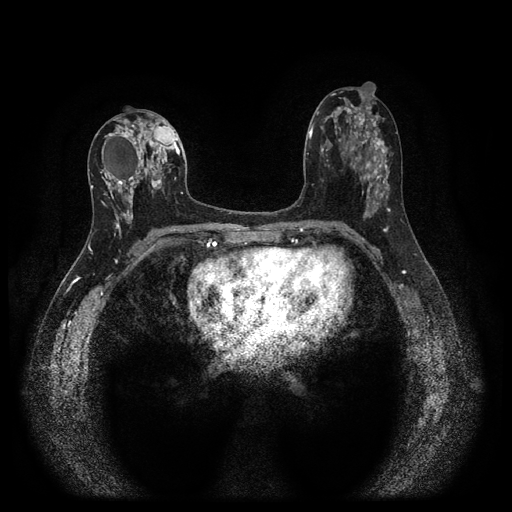
Breast MRI (dynamic contrast-enhanced, multi-phase), one axial slice; slice 52 of 116 in the series (ordered by position); dynamic contrast-enhanced series, time point 2 of 5 at this slice position (early post-contrast); 1.5 T; TE 2.7 ms, TR 5.4 ms; 2 mm slice thickness; 512 × 512 image matrix. Patient: female, 47 years.
Outlined on this slice (semi-automatically segmented with operator editing):
- breast lesion (labelled 'tumour' in the annotation; benign lesions carry a separate 'benign' label): bounding box [x1, y1, x2, y2] px = [94, 113, 178, 228]